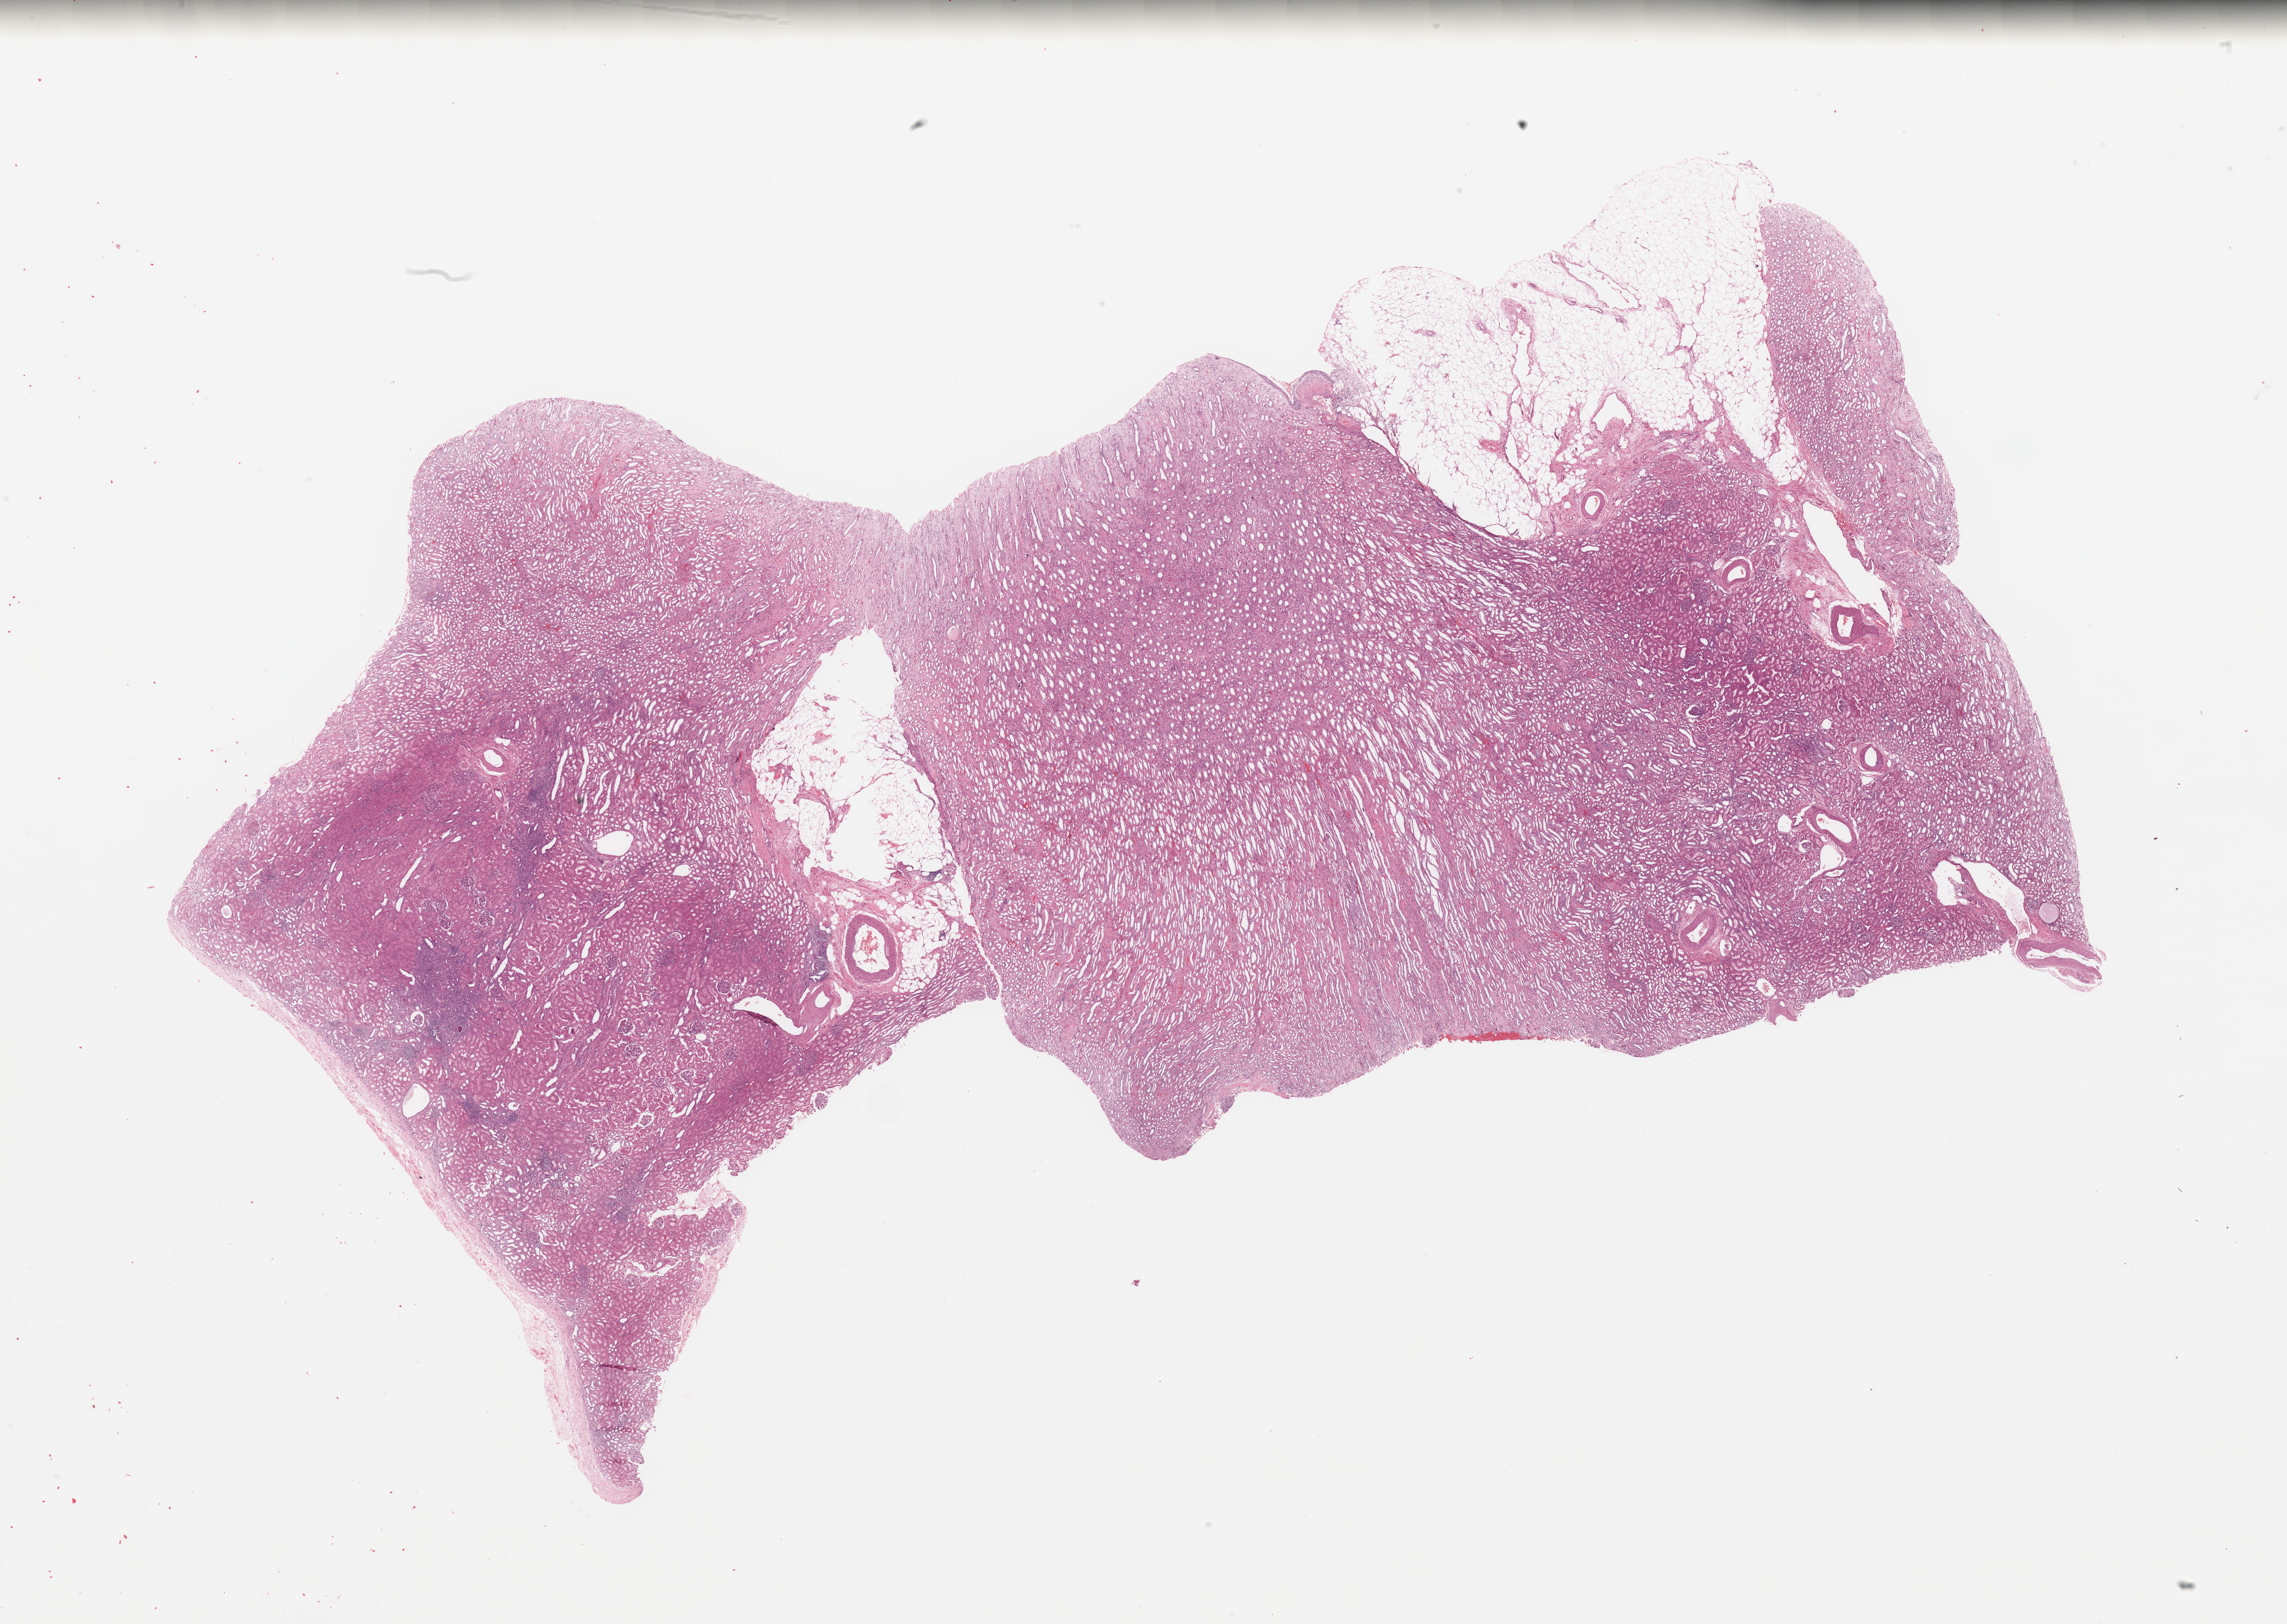
Whole-slide histology image, H&E, a low-resolution overview of the entire scanned area, about 31.5 x 22.4 mm (from a 20x scan); normal (non-tumour) tissue sample, sampled site: kidney. 69-year-old female patient.
* this section: normal (non-tumour) tissue from the same patient
* patient diagnosis: Renal cell carcinoma, NOS